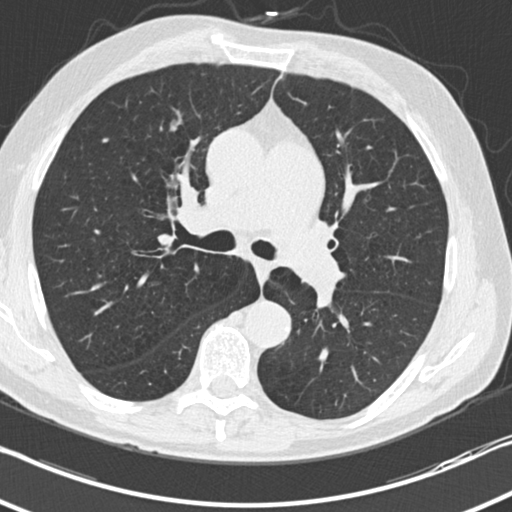
Low-dose screening chest CT, one axial slice. Slice 128 of 212 in the series (ordered by position). 120 kVp. Lung window (W 1500 / L -600 HU). 2 mm slice thickness. 512 × 512 image matrix.
Annotated regions visible in this slice (outlined manually by an expert reader):
- lesion 1 (tumor, upper lobe of right lung): box from (x=171, y=123) to (x=178, y=130) px